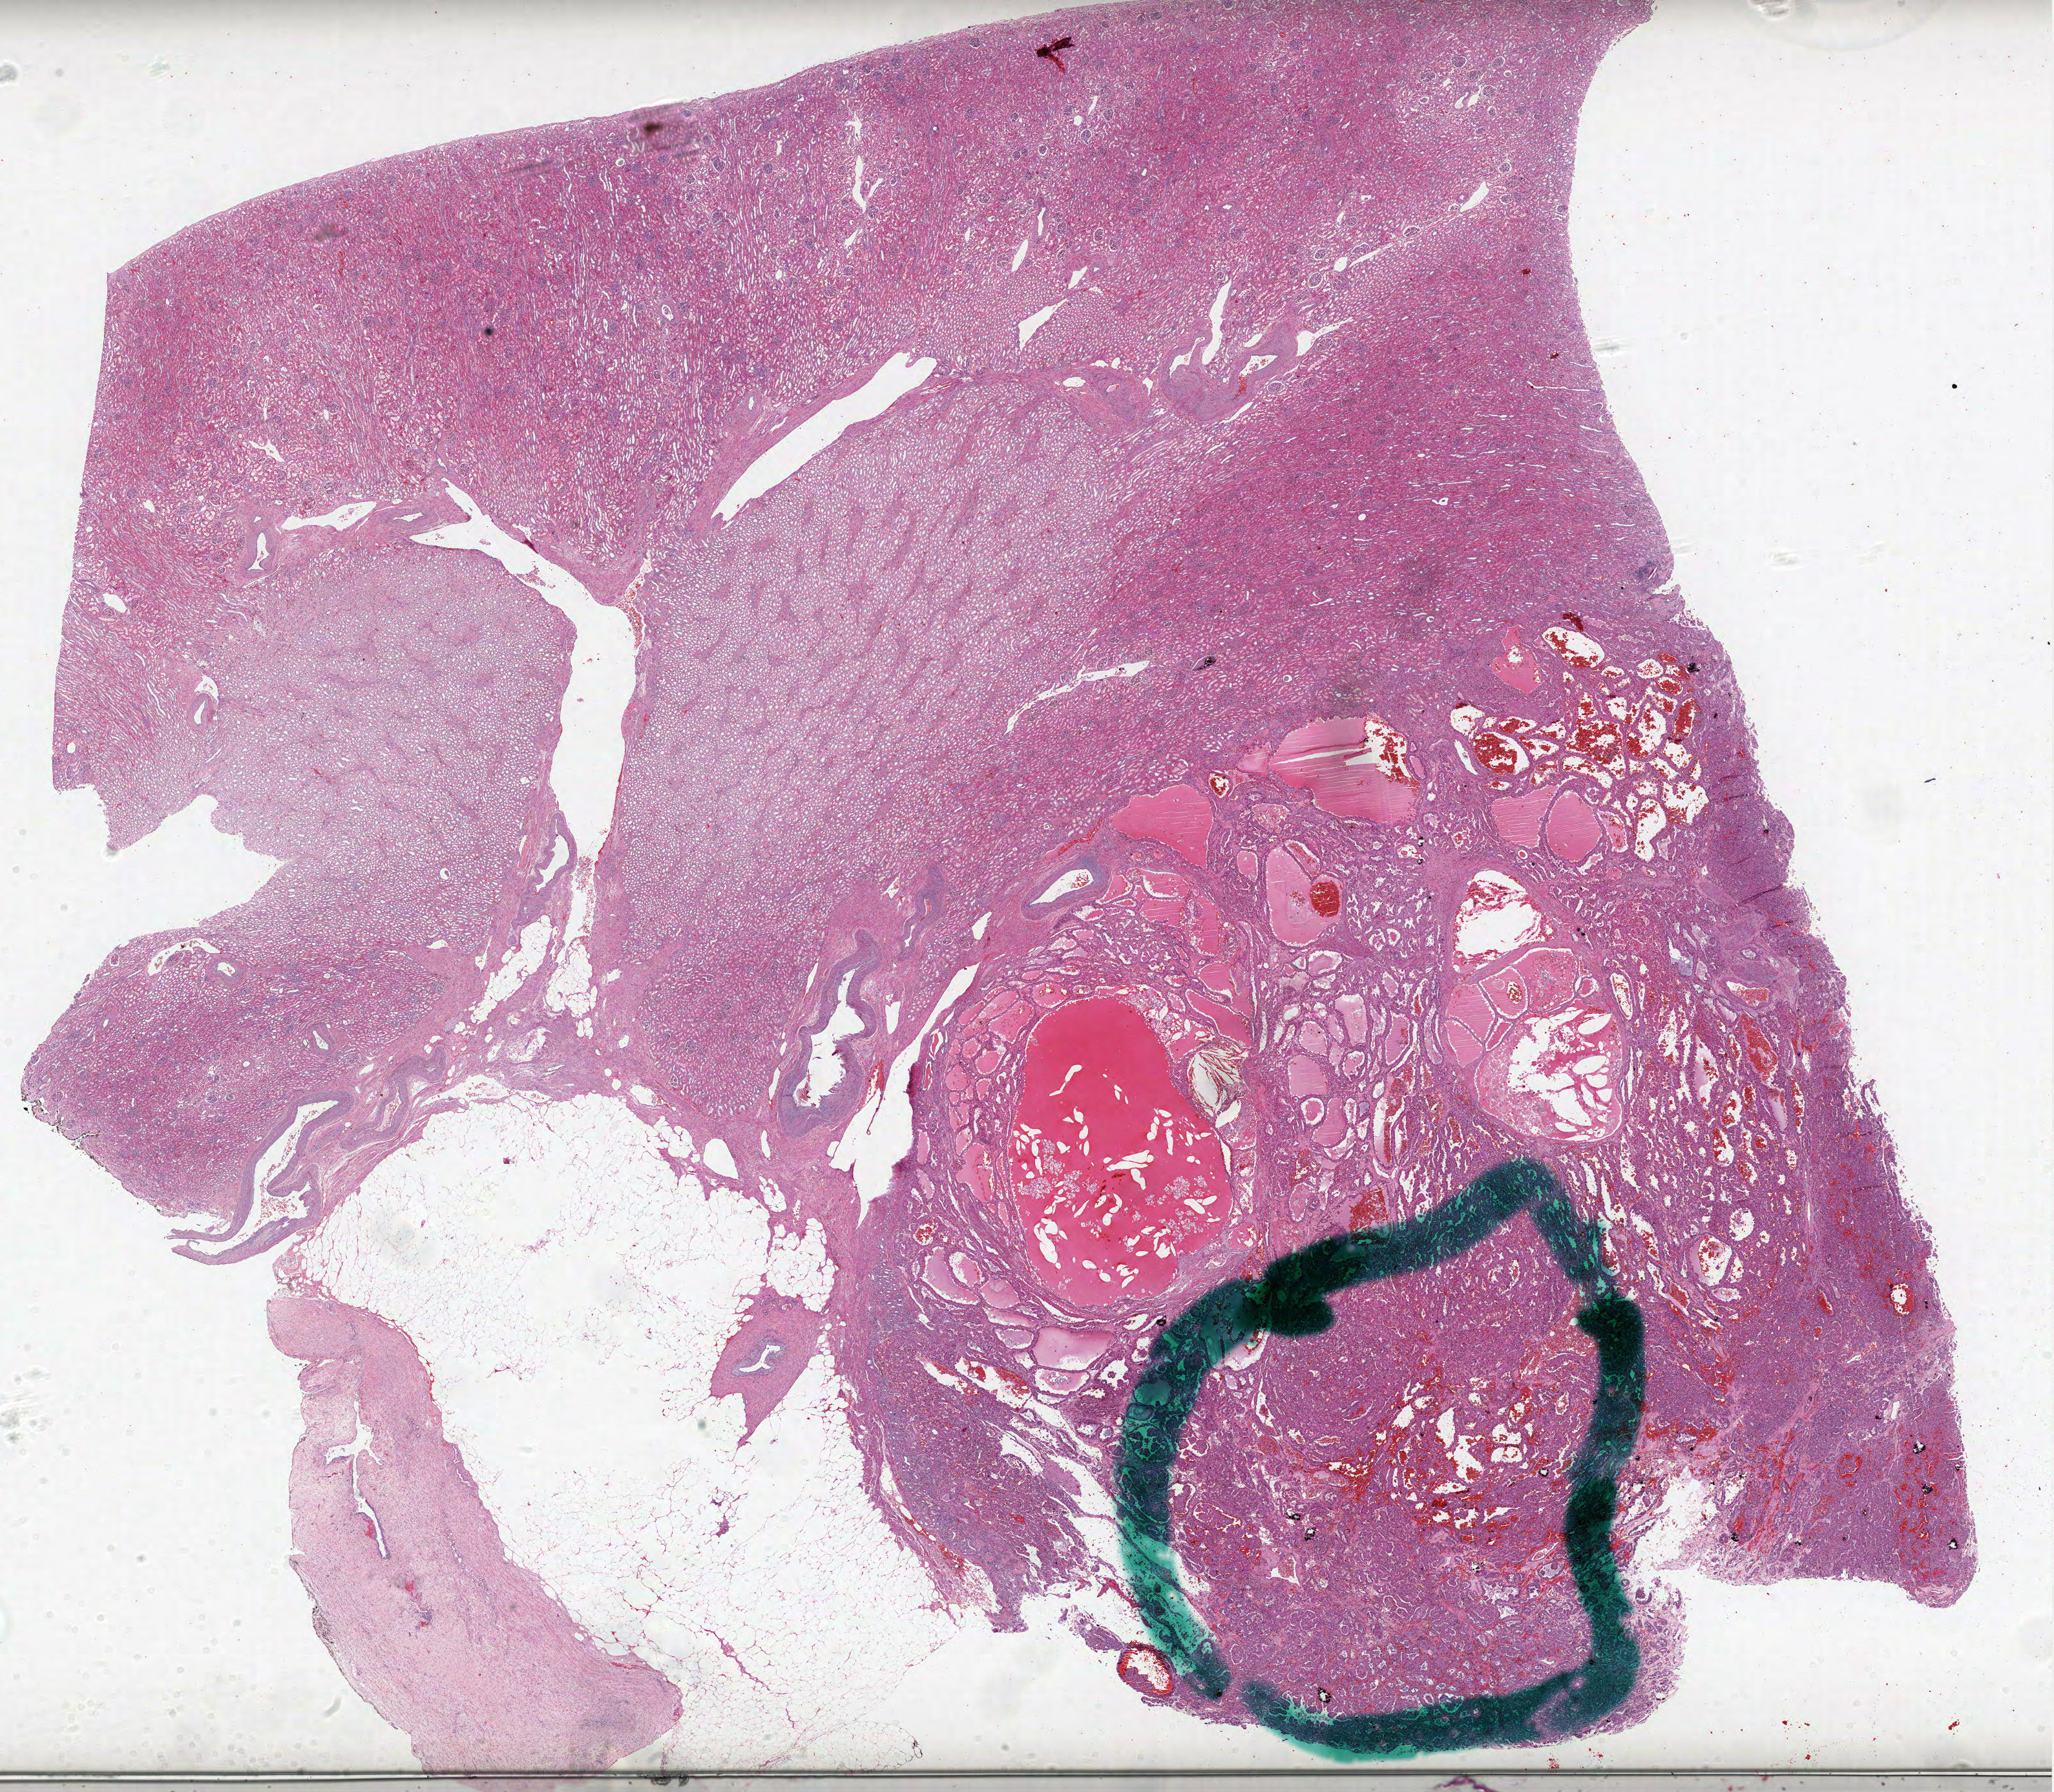
Digitized H&E tissue section (whole slide) — shown as a low-resolution overview of the whole scanned area (about 25.4 x 22.2 mm, slide scanned at 40x); FFPE section; kidney, primary tumour sample. Patient: male, age at initial diagnosis 73 years.
AJCC pathologic stage: I (6th edition). Diagnosis: Papillary adenocarcinoma, NOS.